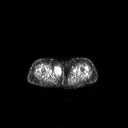
FDG PET of an extremity soft-tissue mass (from a PET/CT study), one axial slice; slice 234 of 311 in the series (ordered by position); 3.27 mm slice thickness; 128 × 128 image matrix, field of view 700 × 700 mm. Patient: female, 78 years. Case-level facts recorded for this patient, not image findings: histological type: leiomyosarcoma; grade: intermediate; site of the primary tumour: parascapusular.
Structures marked on this image (expert contour drawn on MRI and transferred to this co-registered scan by the dataset authors):
- gross tumour volume including surrounding oedema: bounding box [x1, y1, x2, y2] px = [53, 65, 62, 76]
- gross tumour volume (mass): [53, 65, 62, 76]